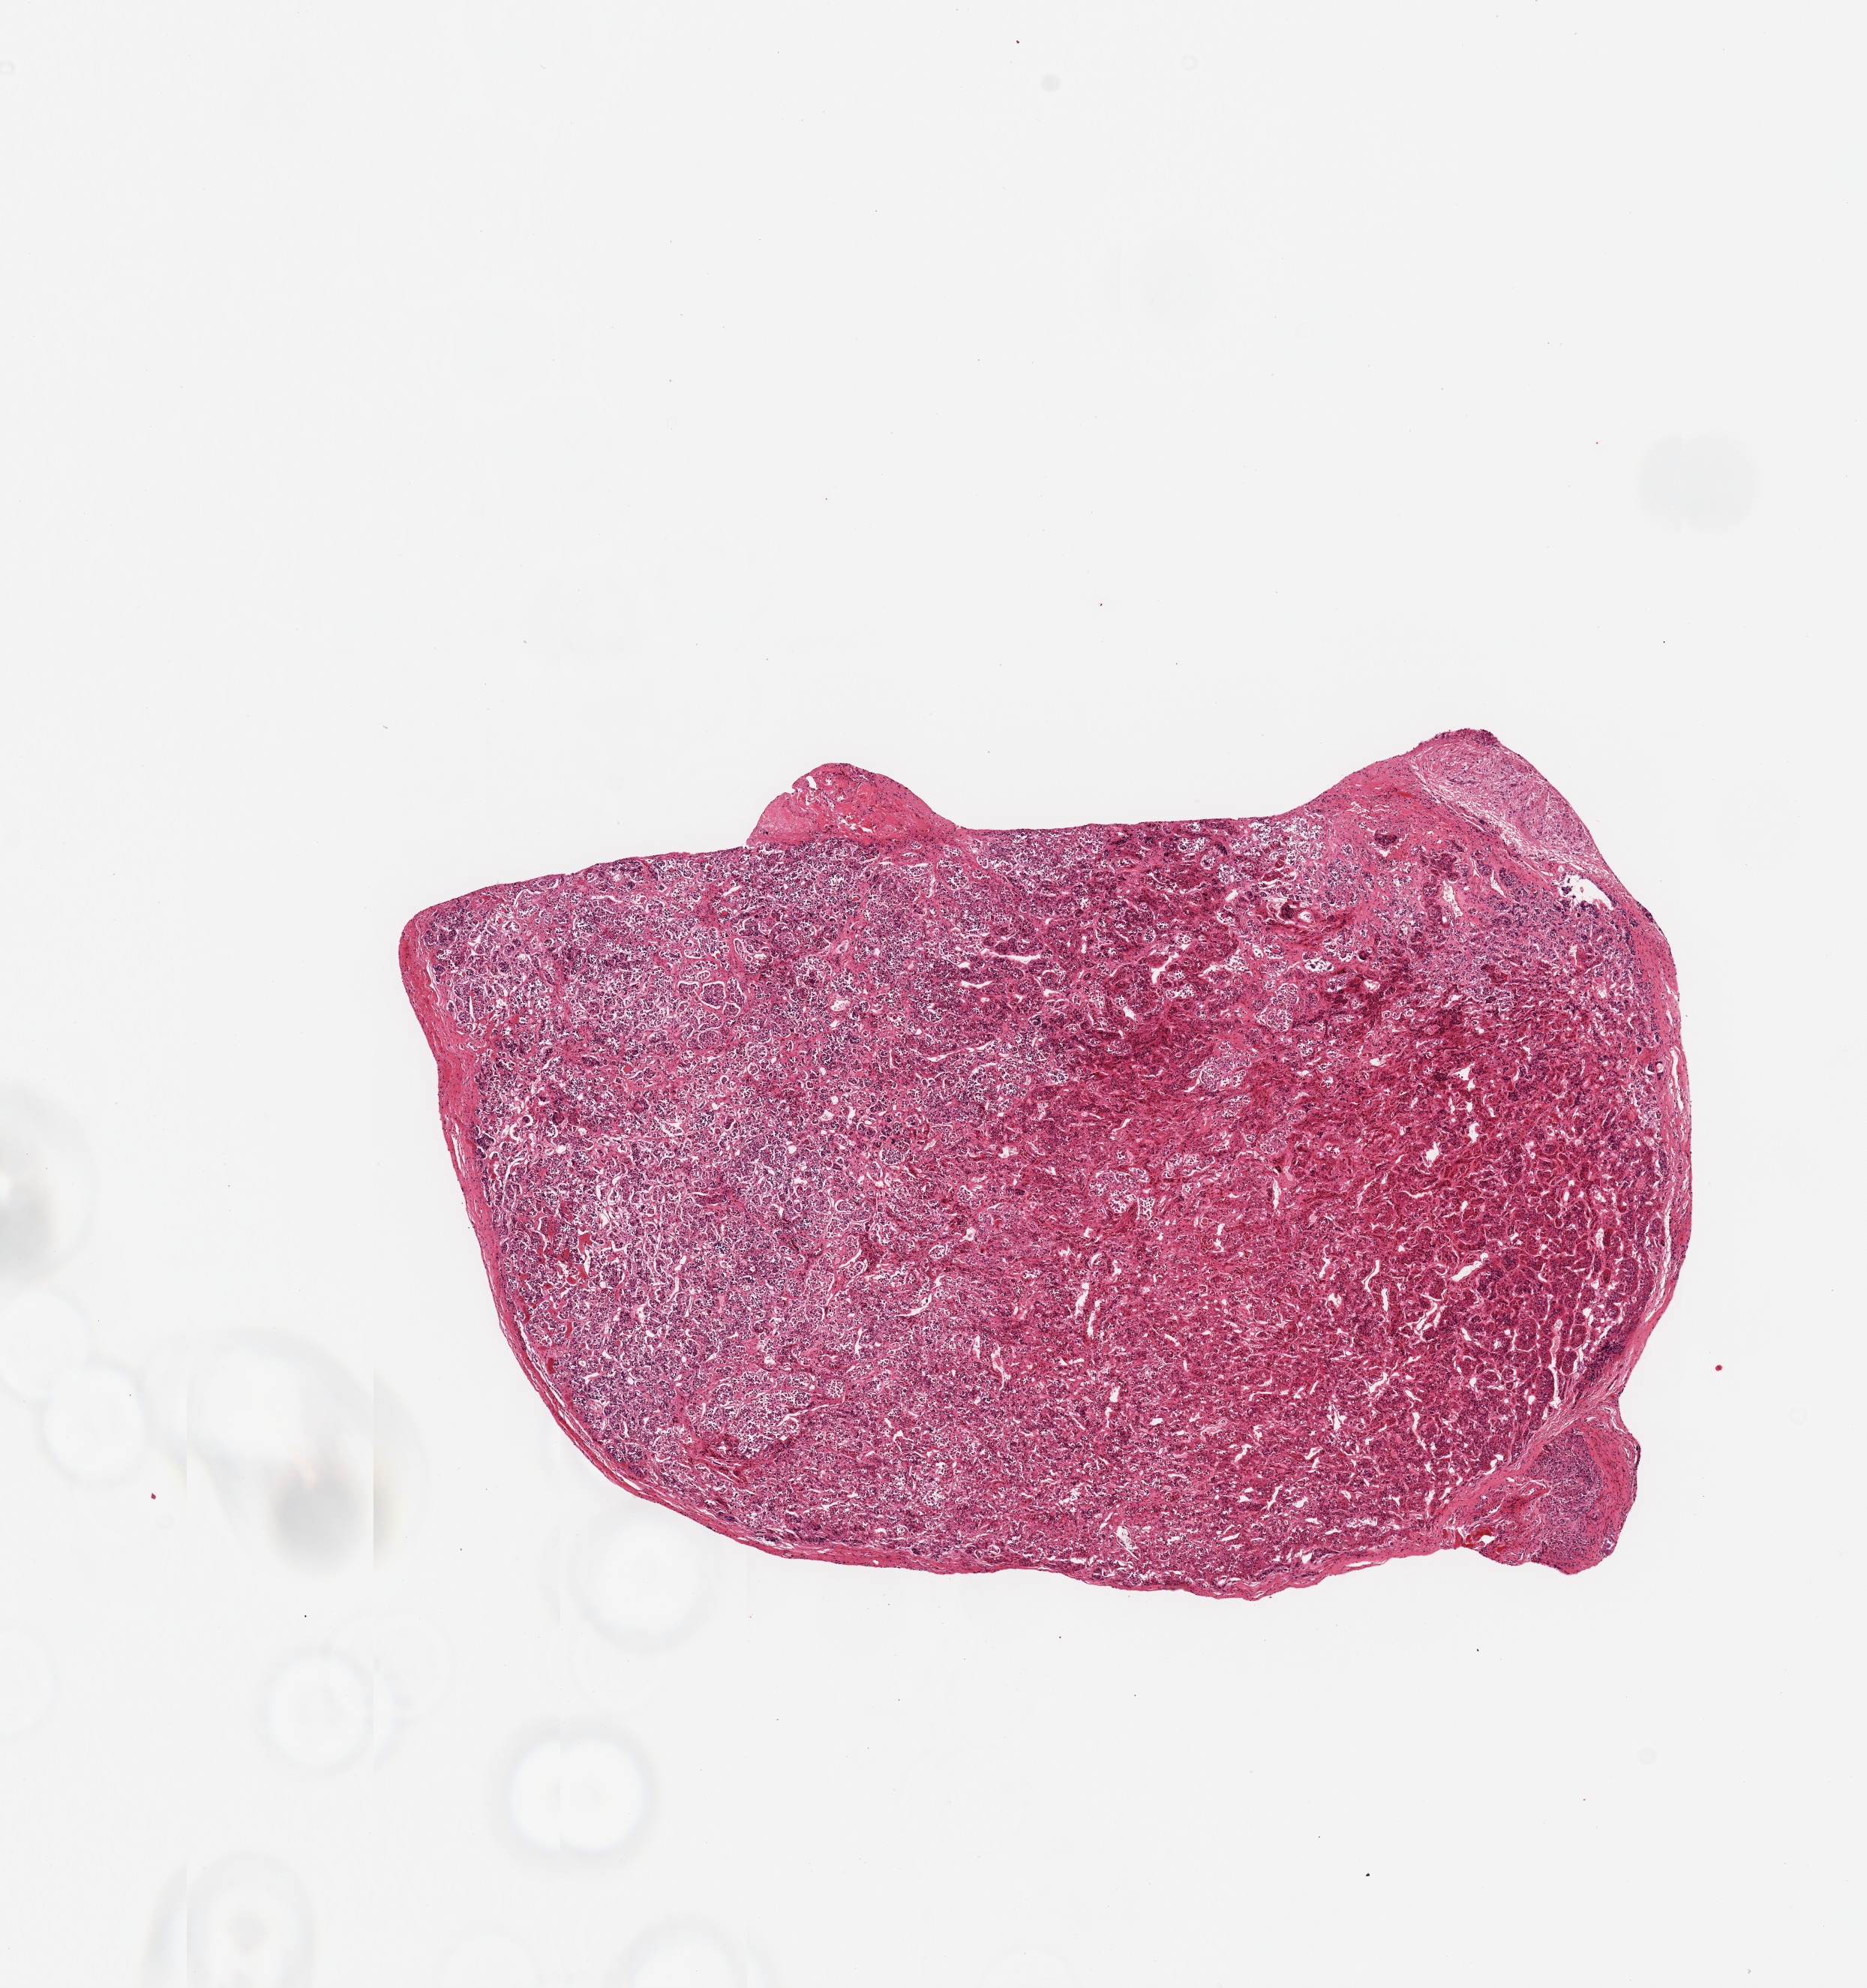
Digitized haematoxylin and eosin-stained section, low-resolution overview of the scanned area, about 9.8 x 10.5 mm (slide scanned at 20x), PAXgene-fixed, paraffin-embedded tissue, sampled site (target tissue): pituitary, tissue donor sample. Donor: male.
• review note (as recorded): 1 piece; predominantly adenohypophysis, small portion of neurohypophysis